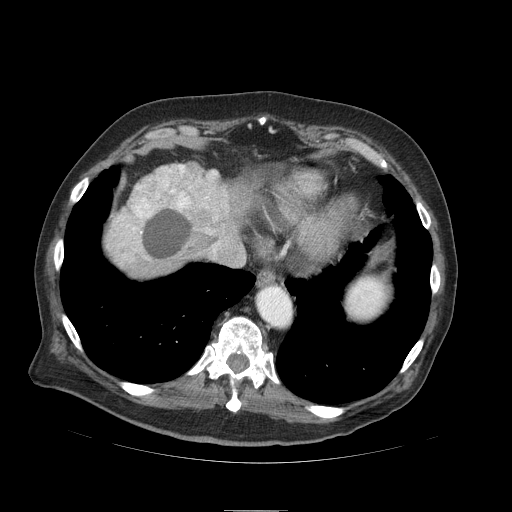
Contrast-enhanced abdominal CT (liver protocol), one axial slice. Position 80 of 103 along the scan axis. Reconstruction kernel STANDARD. 120 kVp. Soft-tissue window (W 400 / L 40 HU). 512 × 512 image matrix. From the clinical record (not read from this slice): diagnosis: hepatocellular carcinoma (patient treated with transarterial chemoembolisation; whether this scan precedes or follows treatment is not stated here); TNM stage (as recorded): Stage-IIIA; Child-Pugh class: B; tumour differentiation: well differentiated; tumour size: 13 cm.
Structures marked on this image (semi-automatically segmented with operator editing):
- liver parenchyma outside the tumour (the mass and vessels are separate outlines, so this box may not span the whole liver): box from (x=104, y=164) to (x=262, y=276) px
- mass: (x=110, y=165)–(x=227, y=262)
- liver vessels: (x=213, y=172)–(x=216, y=175)